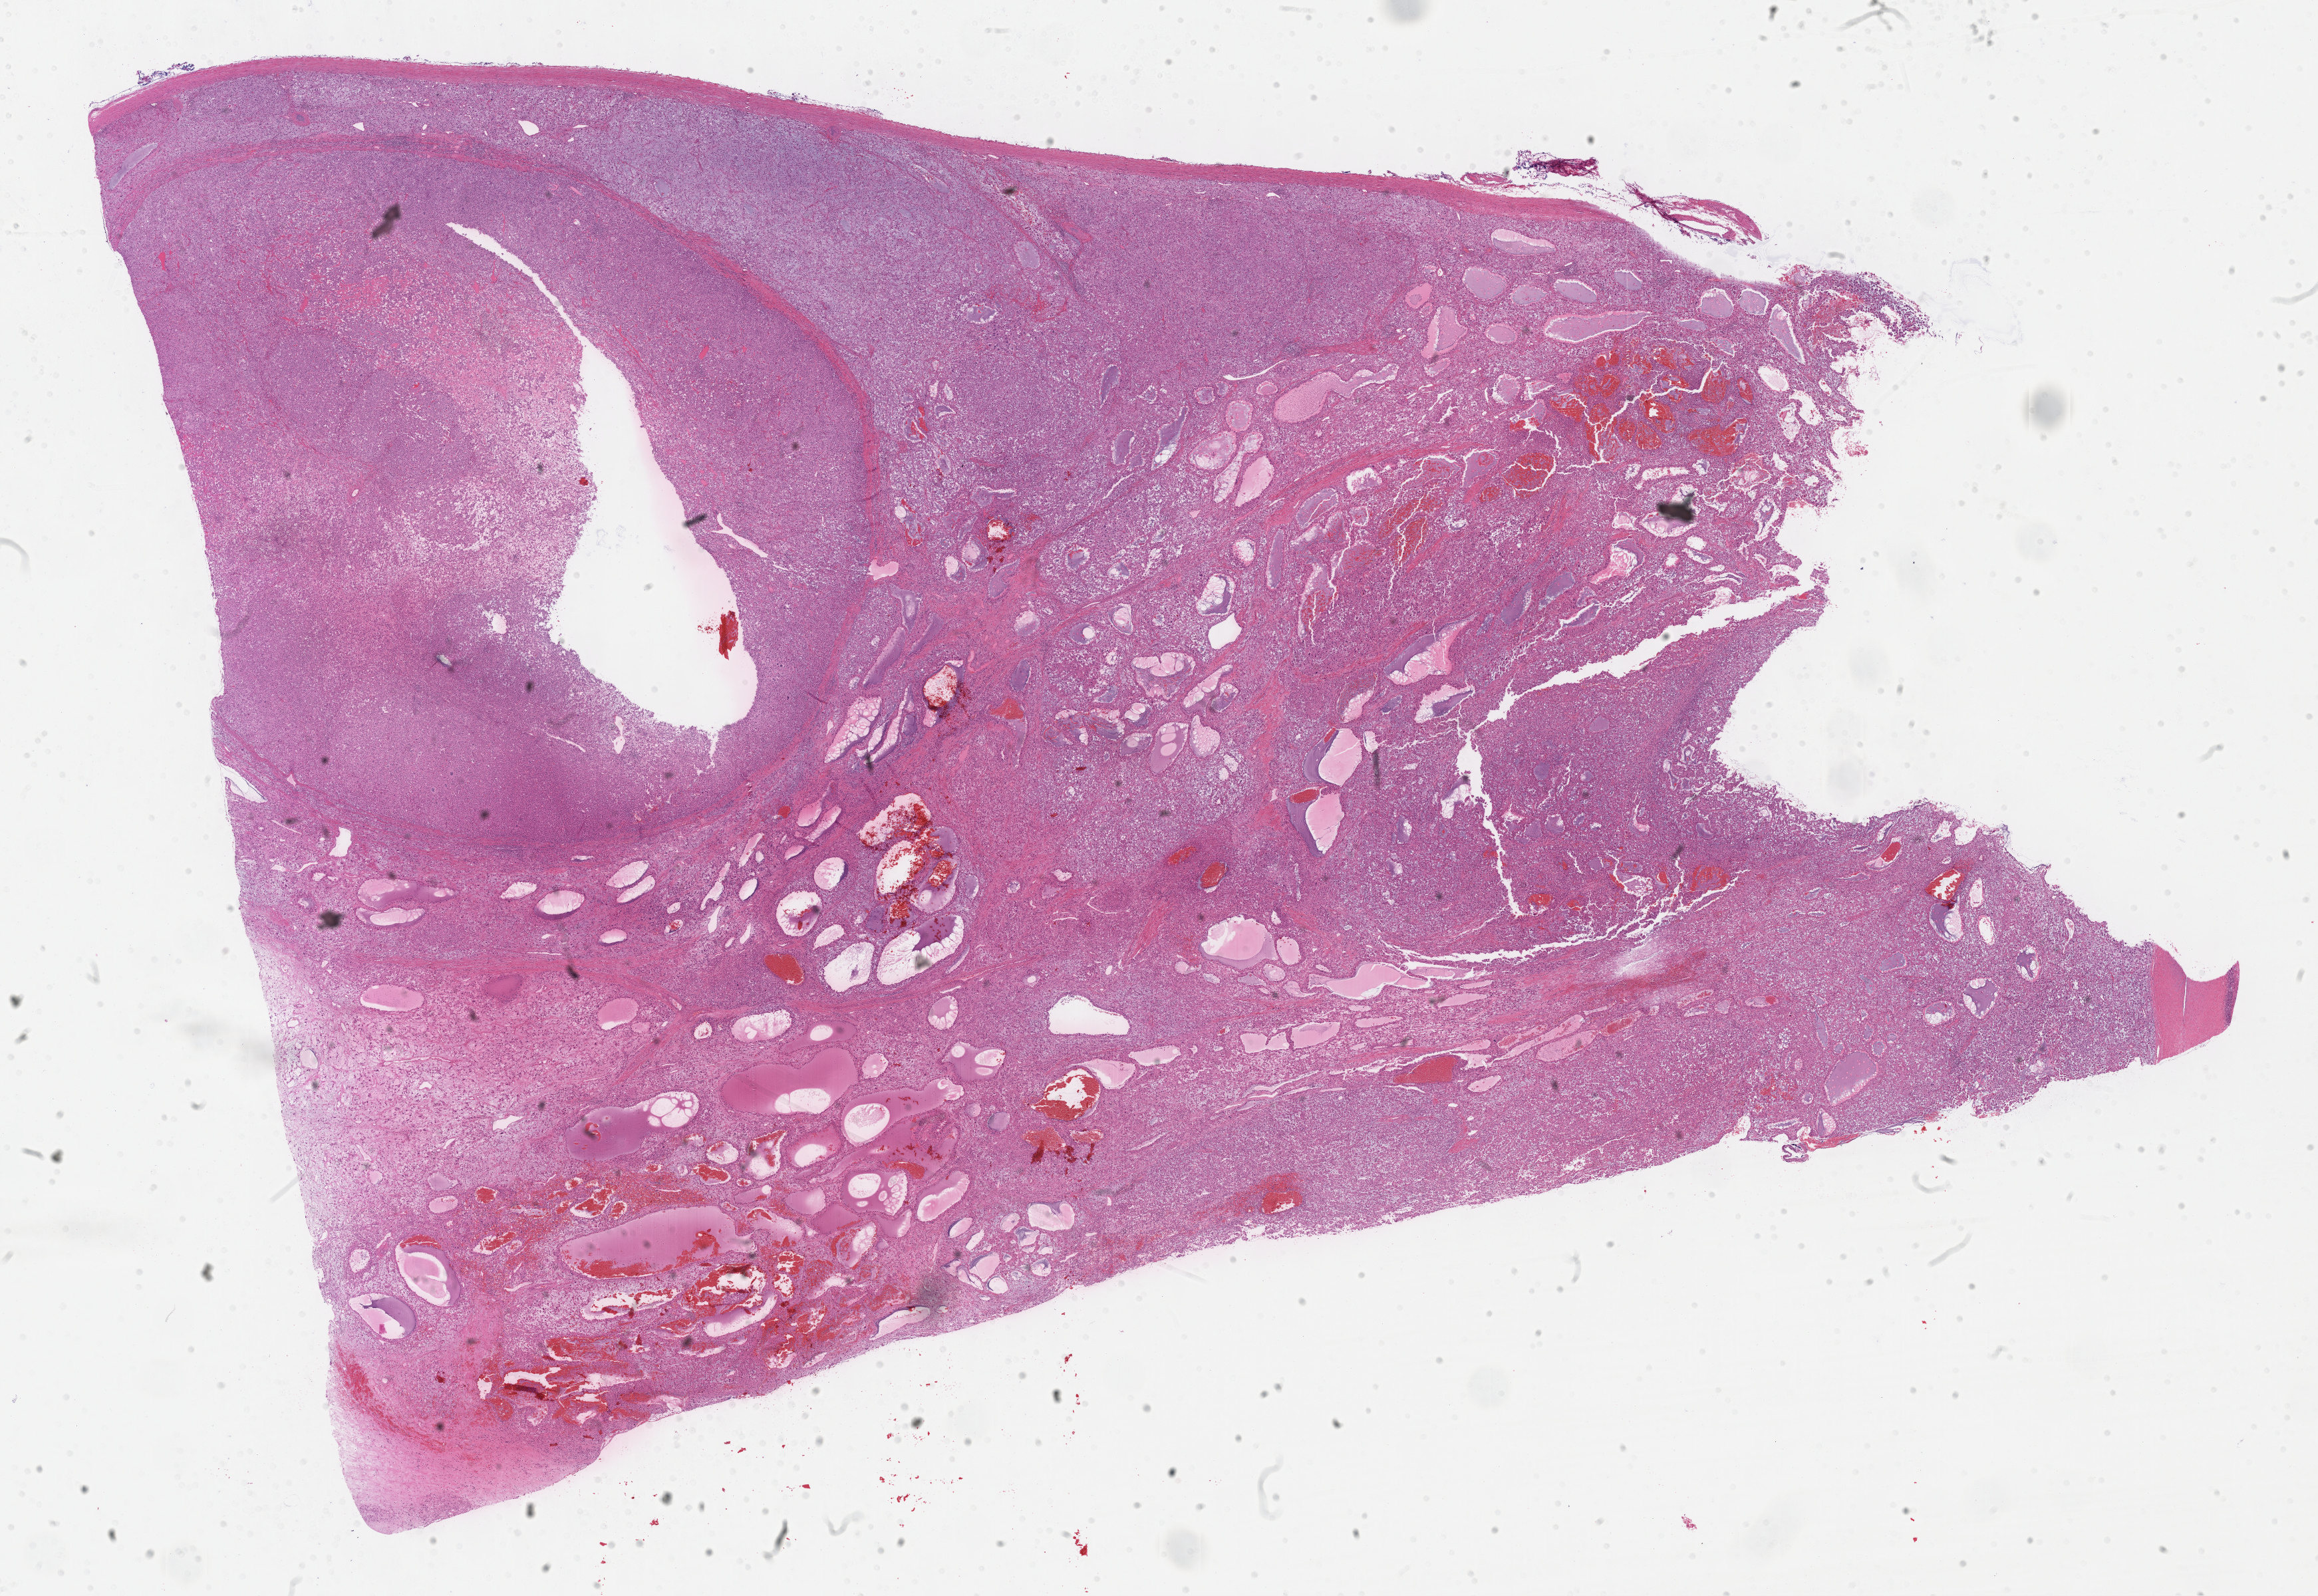
Whole-slide histology image, Hematoxylin and eosin (H&E) stained — shown as a low-resolution overview of the whole scanned area (about 28.2 x 19.4 mm). Formalin-fixed paraffin-embedded (FFPE) diagnostic section. Primary tumour sample from the adrenal cortex. Patient: female, age at initial diagnosis 26 years.
* diagnosis: Adrenal cortical carcinoma (cortex of adrenal gland)